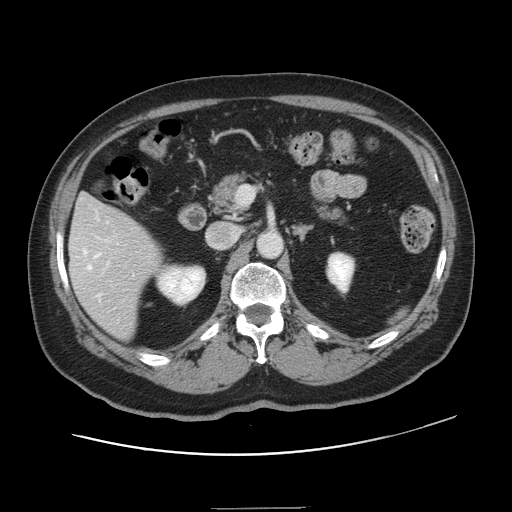
Contrast-enhanced abdominal CT, one axial slice; slice 71 of 143 in the series (ordered by position); 120 kVp; intravenous contrast given; soft-tissue window (W 400 / L 40 HU); 512 × 512 image matrix. Male patient, age 62 years. From the clinical record (not read from this slice): diagnosis: colorectal cancer liver metastases, imaged before liver resection; multiple liver metastases: yes; largest metastasis: 2.7 cm; disease in both lobes: no.
Annotated regions visible in this slice (outlined manually by an expert reader):
- hepatic veins: bounding box (x1, y1, x2, y2) in pixels: (83, 222, 108, 299)
- liver: (70, 195, 161, 339)
- planned liver remnant (the part of the liver to remain after resection): (75, 195, 119, 221)
- portal vein (with intrahepatic branches): (105, 240, 110, 264)